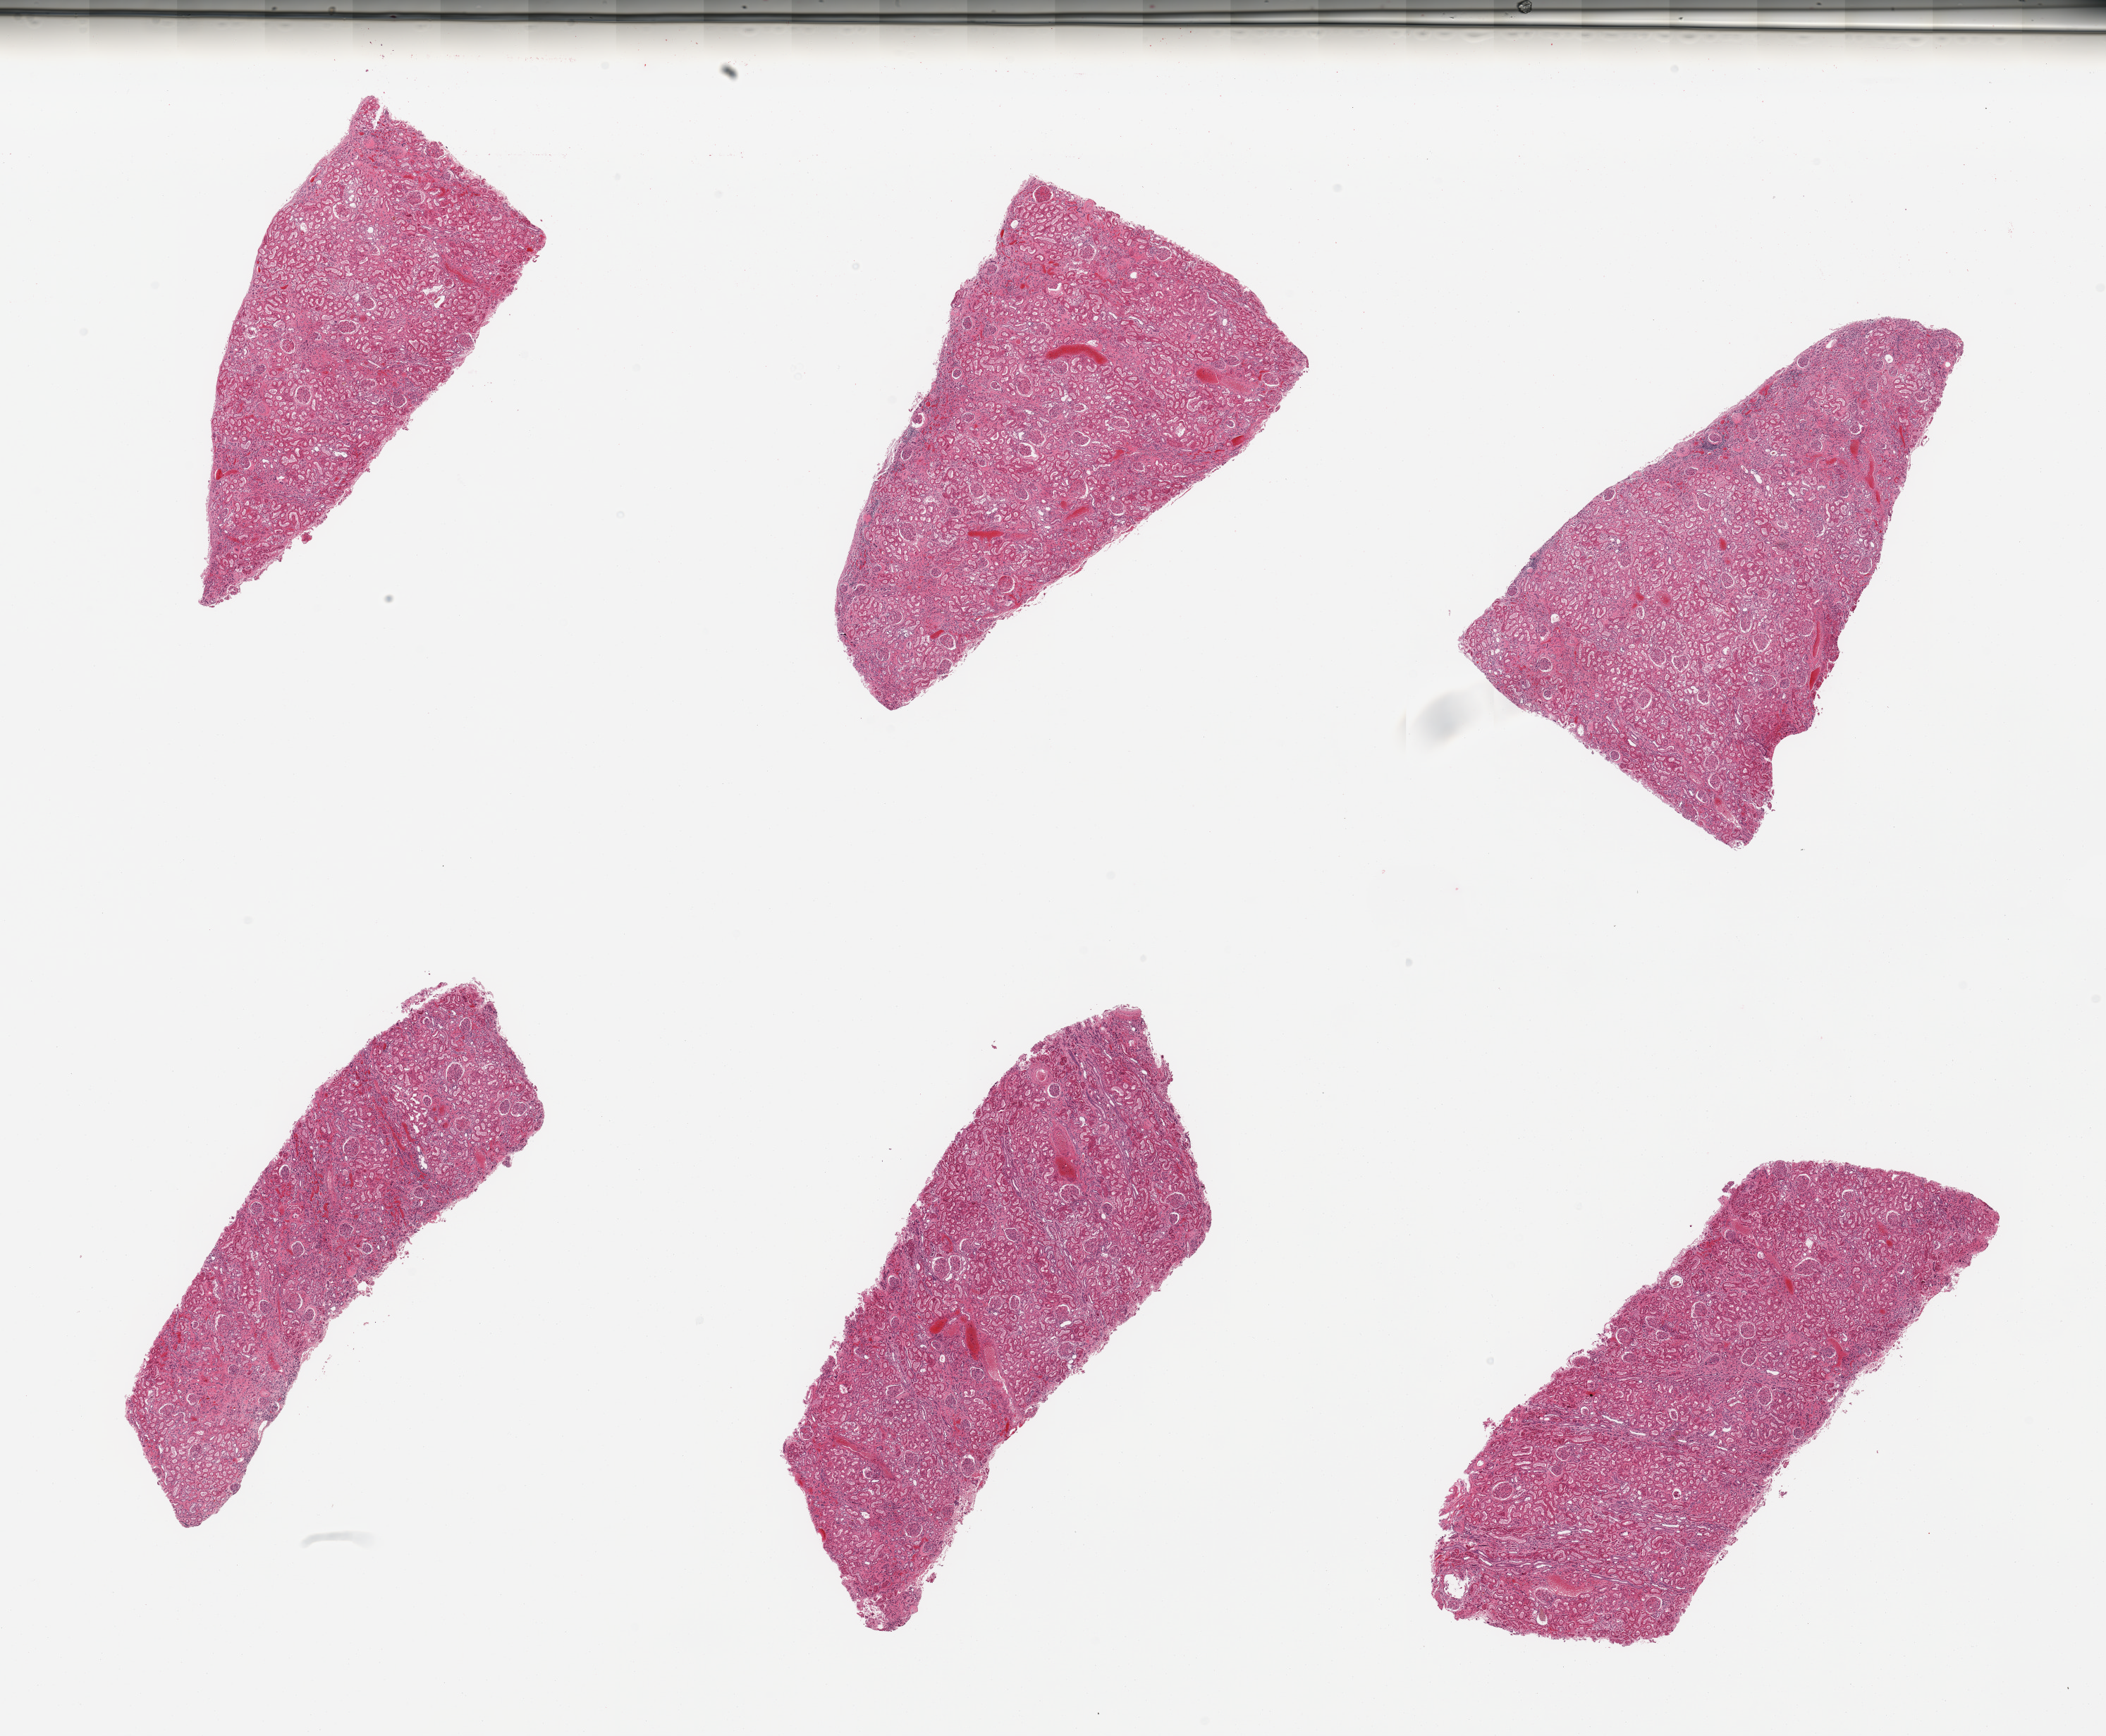
Whole-slide image, haematoxylin and eosin stain, a low-resolution overview of the entire scanned area, about 23.6 x 19.5 mm (acquisition: 20x scan), PAXgene-fixed, paraffin-embedded tissue, sampled site (target tissue): renal cortex, tissue donor sample. Donor sex: female.
Review note (as recorded): 6 pieces, glomeruli present; tubules well preserved.